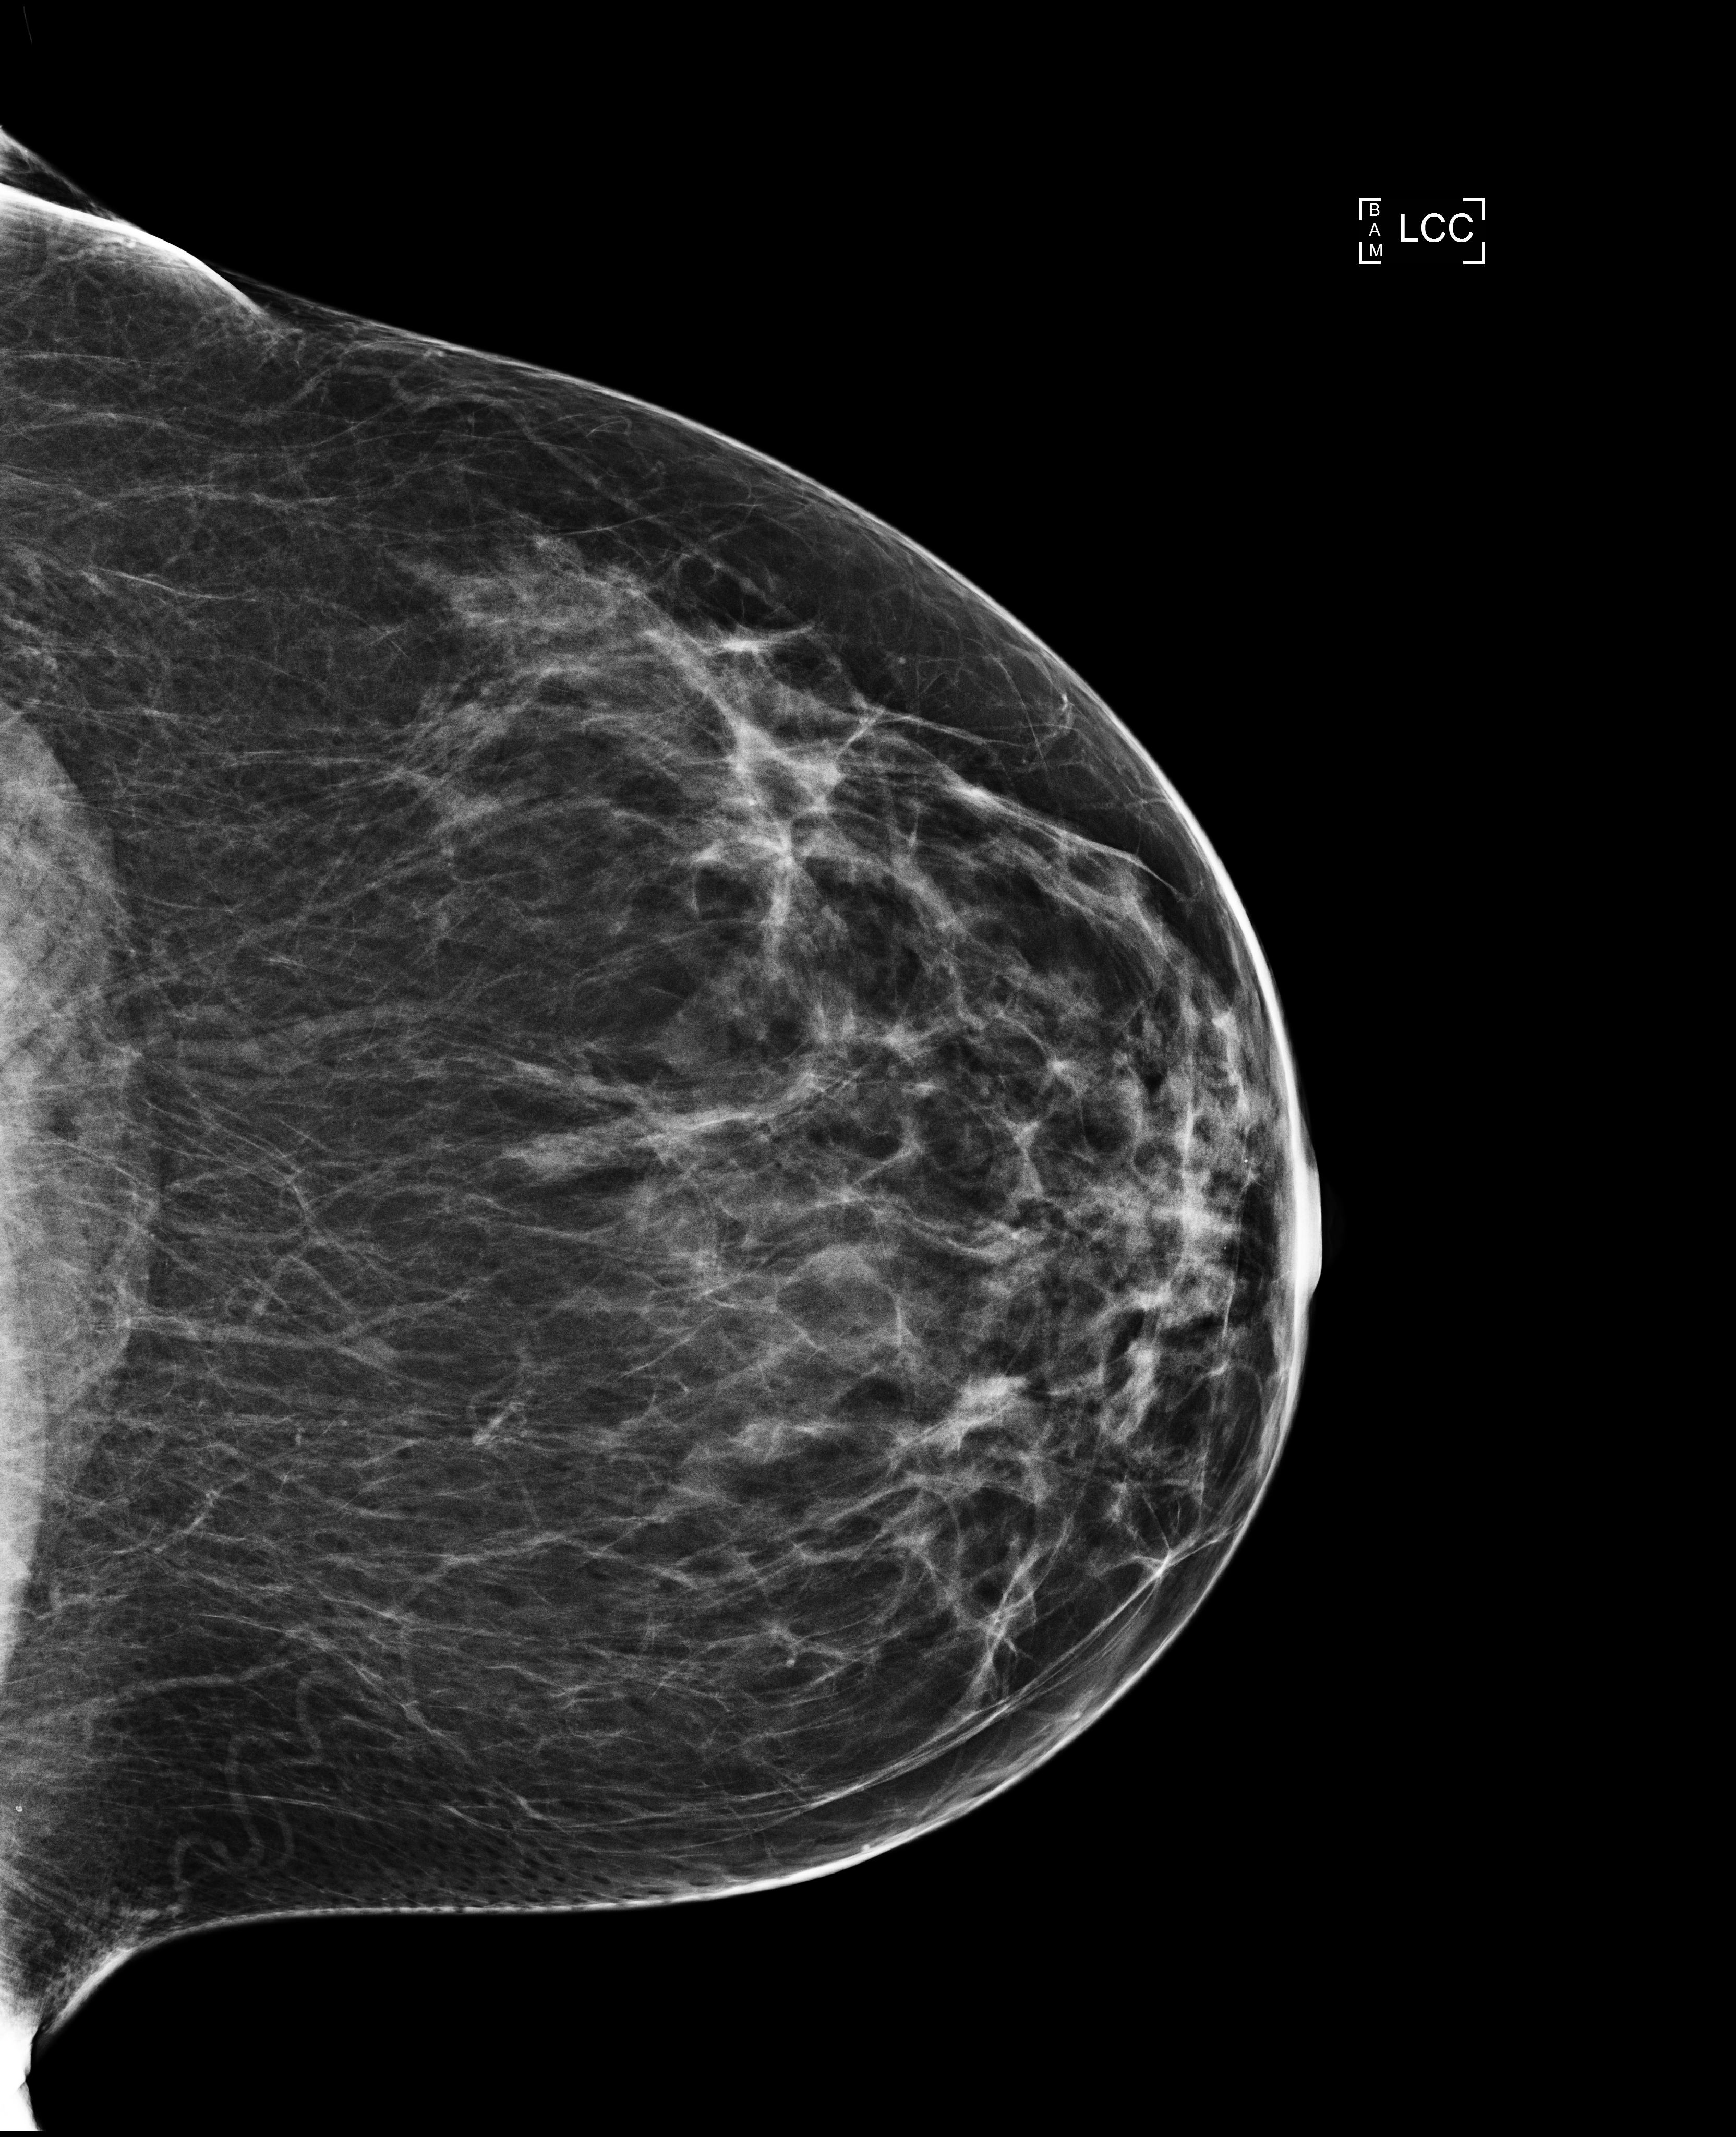
Screening examination. Patient: female, 47 years.
Image type: full-field digital mammogram. Breast: left. Projection: cranio-caudal projection.